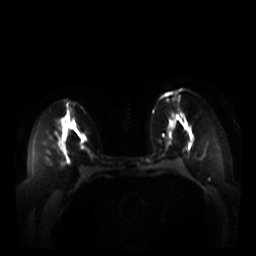
Breast MRI, one axial slice; position 19 of 44 along the scan axis; diffusion-weighted series; image 2 of 4 stored at this slice position (different b-values; order by instance number); 3 T; 5 mm slice thickness; 256 × 256 image matrix. Female patient.
Outlined on this slice (outlined manually by an expert reader):
- tumour on diffusion-weighted imaging: bounding box [x1, y1, x2, y2] px = [190, 133, 193, 138]